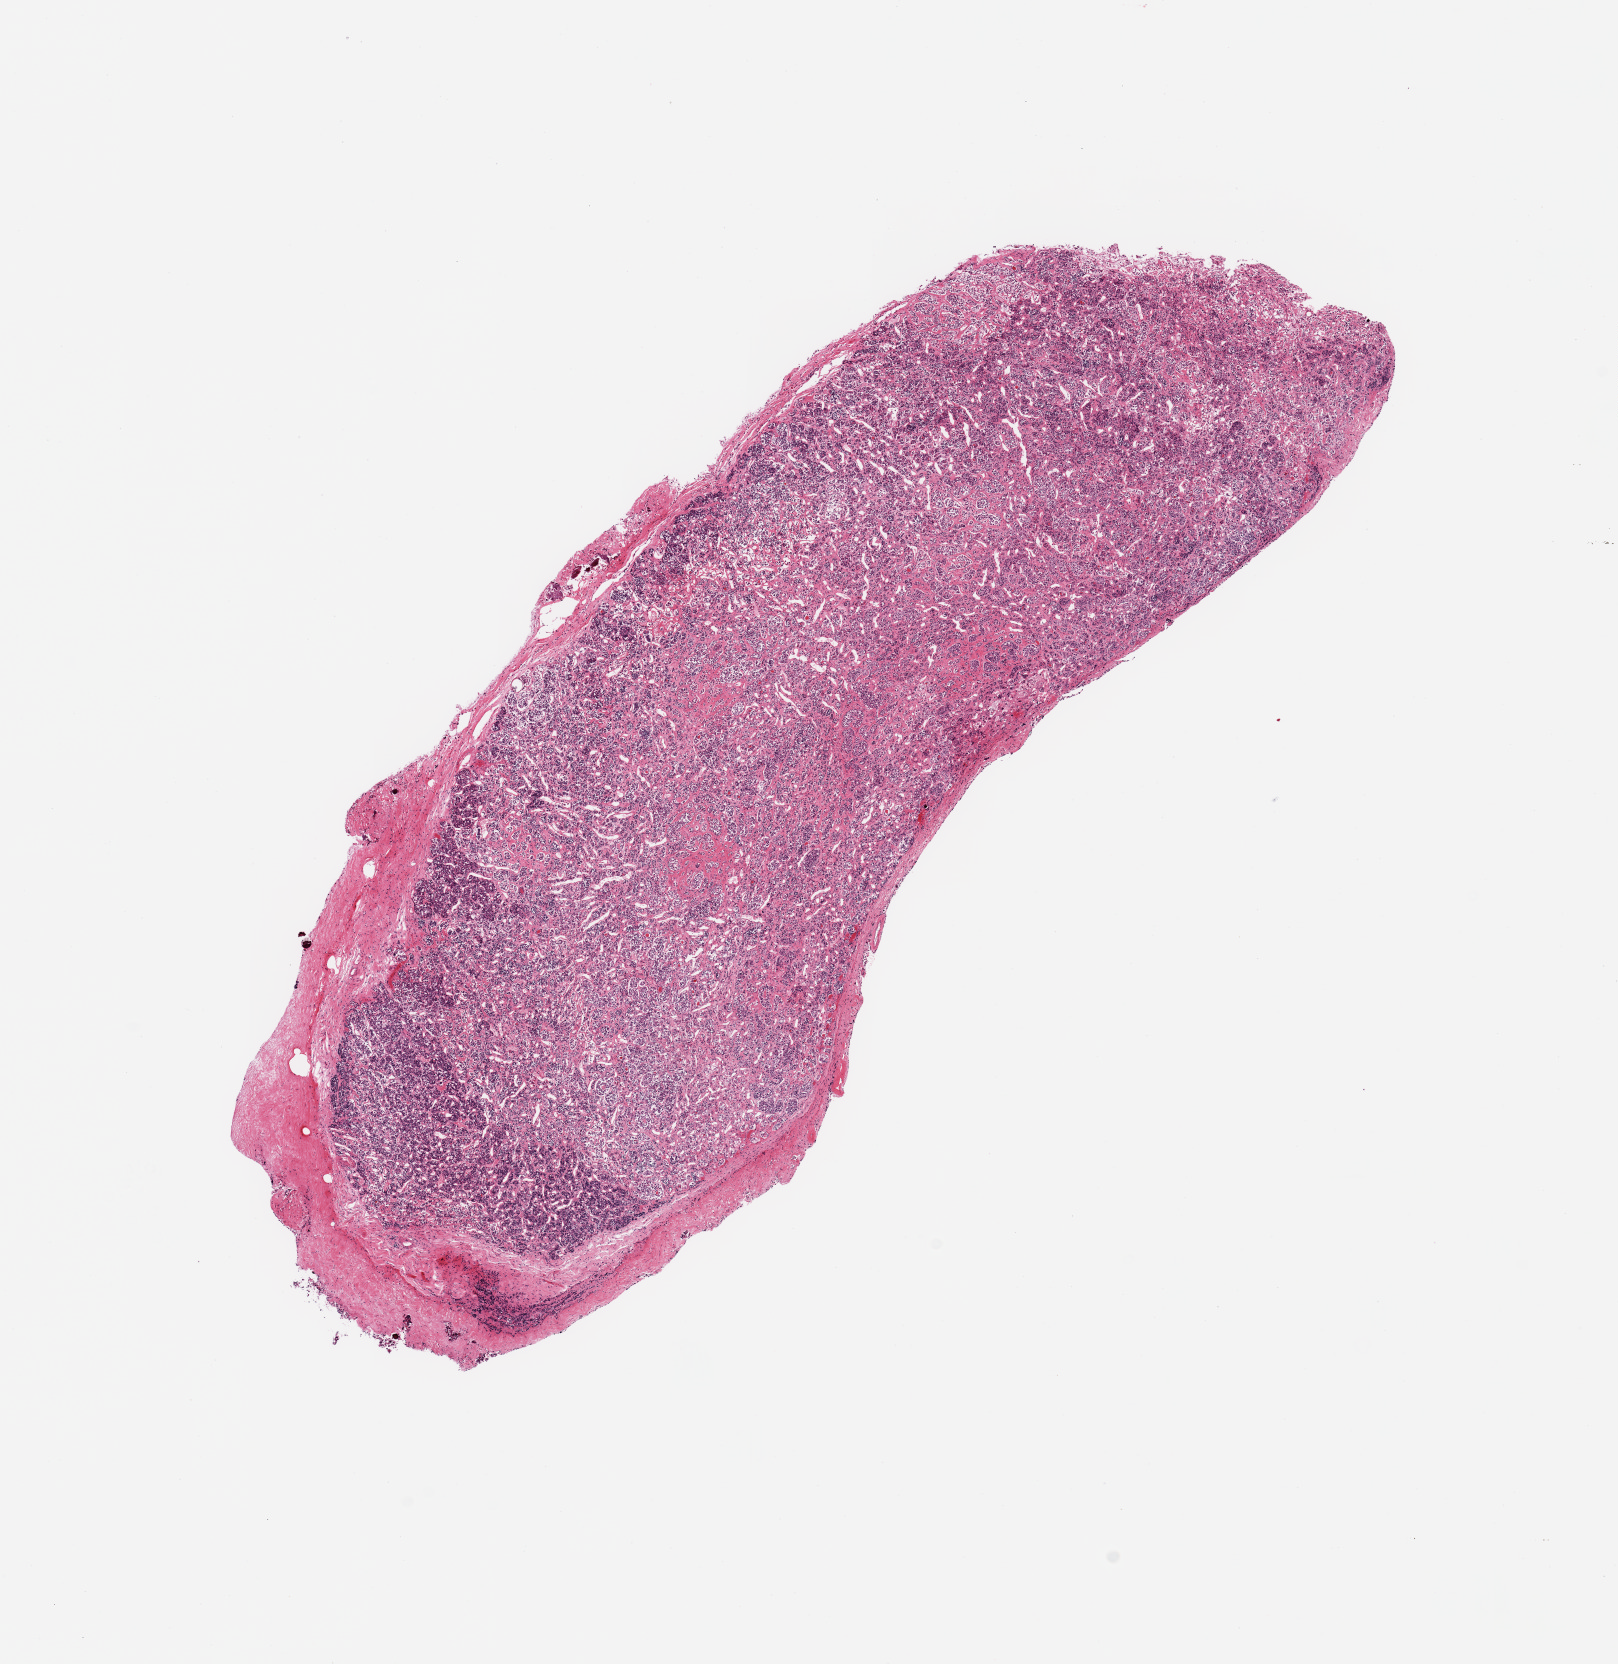
Whole-slide image, H&E stain, brightfield — whole scanned area (about 12.8 x 13.2 mm, acquisition: 20x scan) shown as a low-resolution overview, PAXgene-fixed, paraffin-embedded tissue, section of pituitary (target tissue), tissue donor sample. Female donor.
- pathologist's review note for this sample: 1 piece; anterior pituitary (not brain cortex)